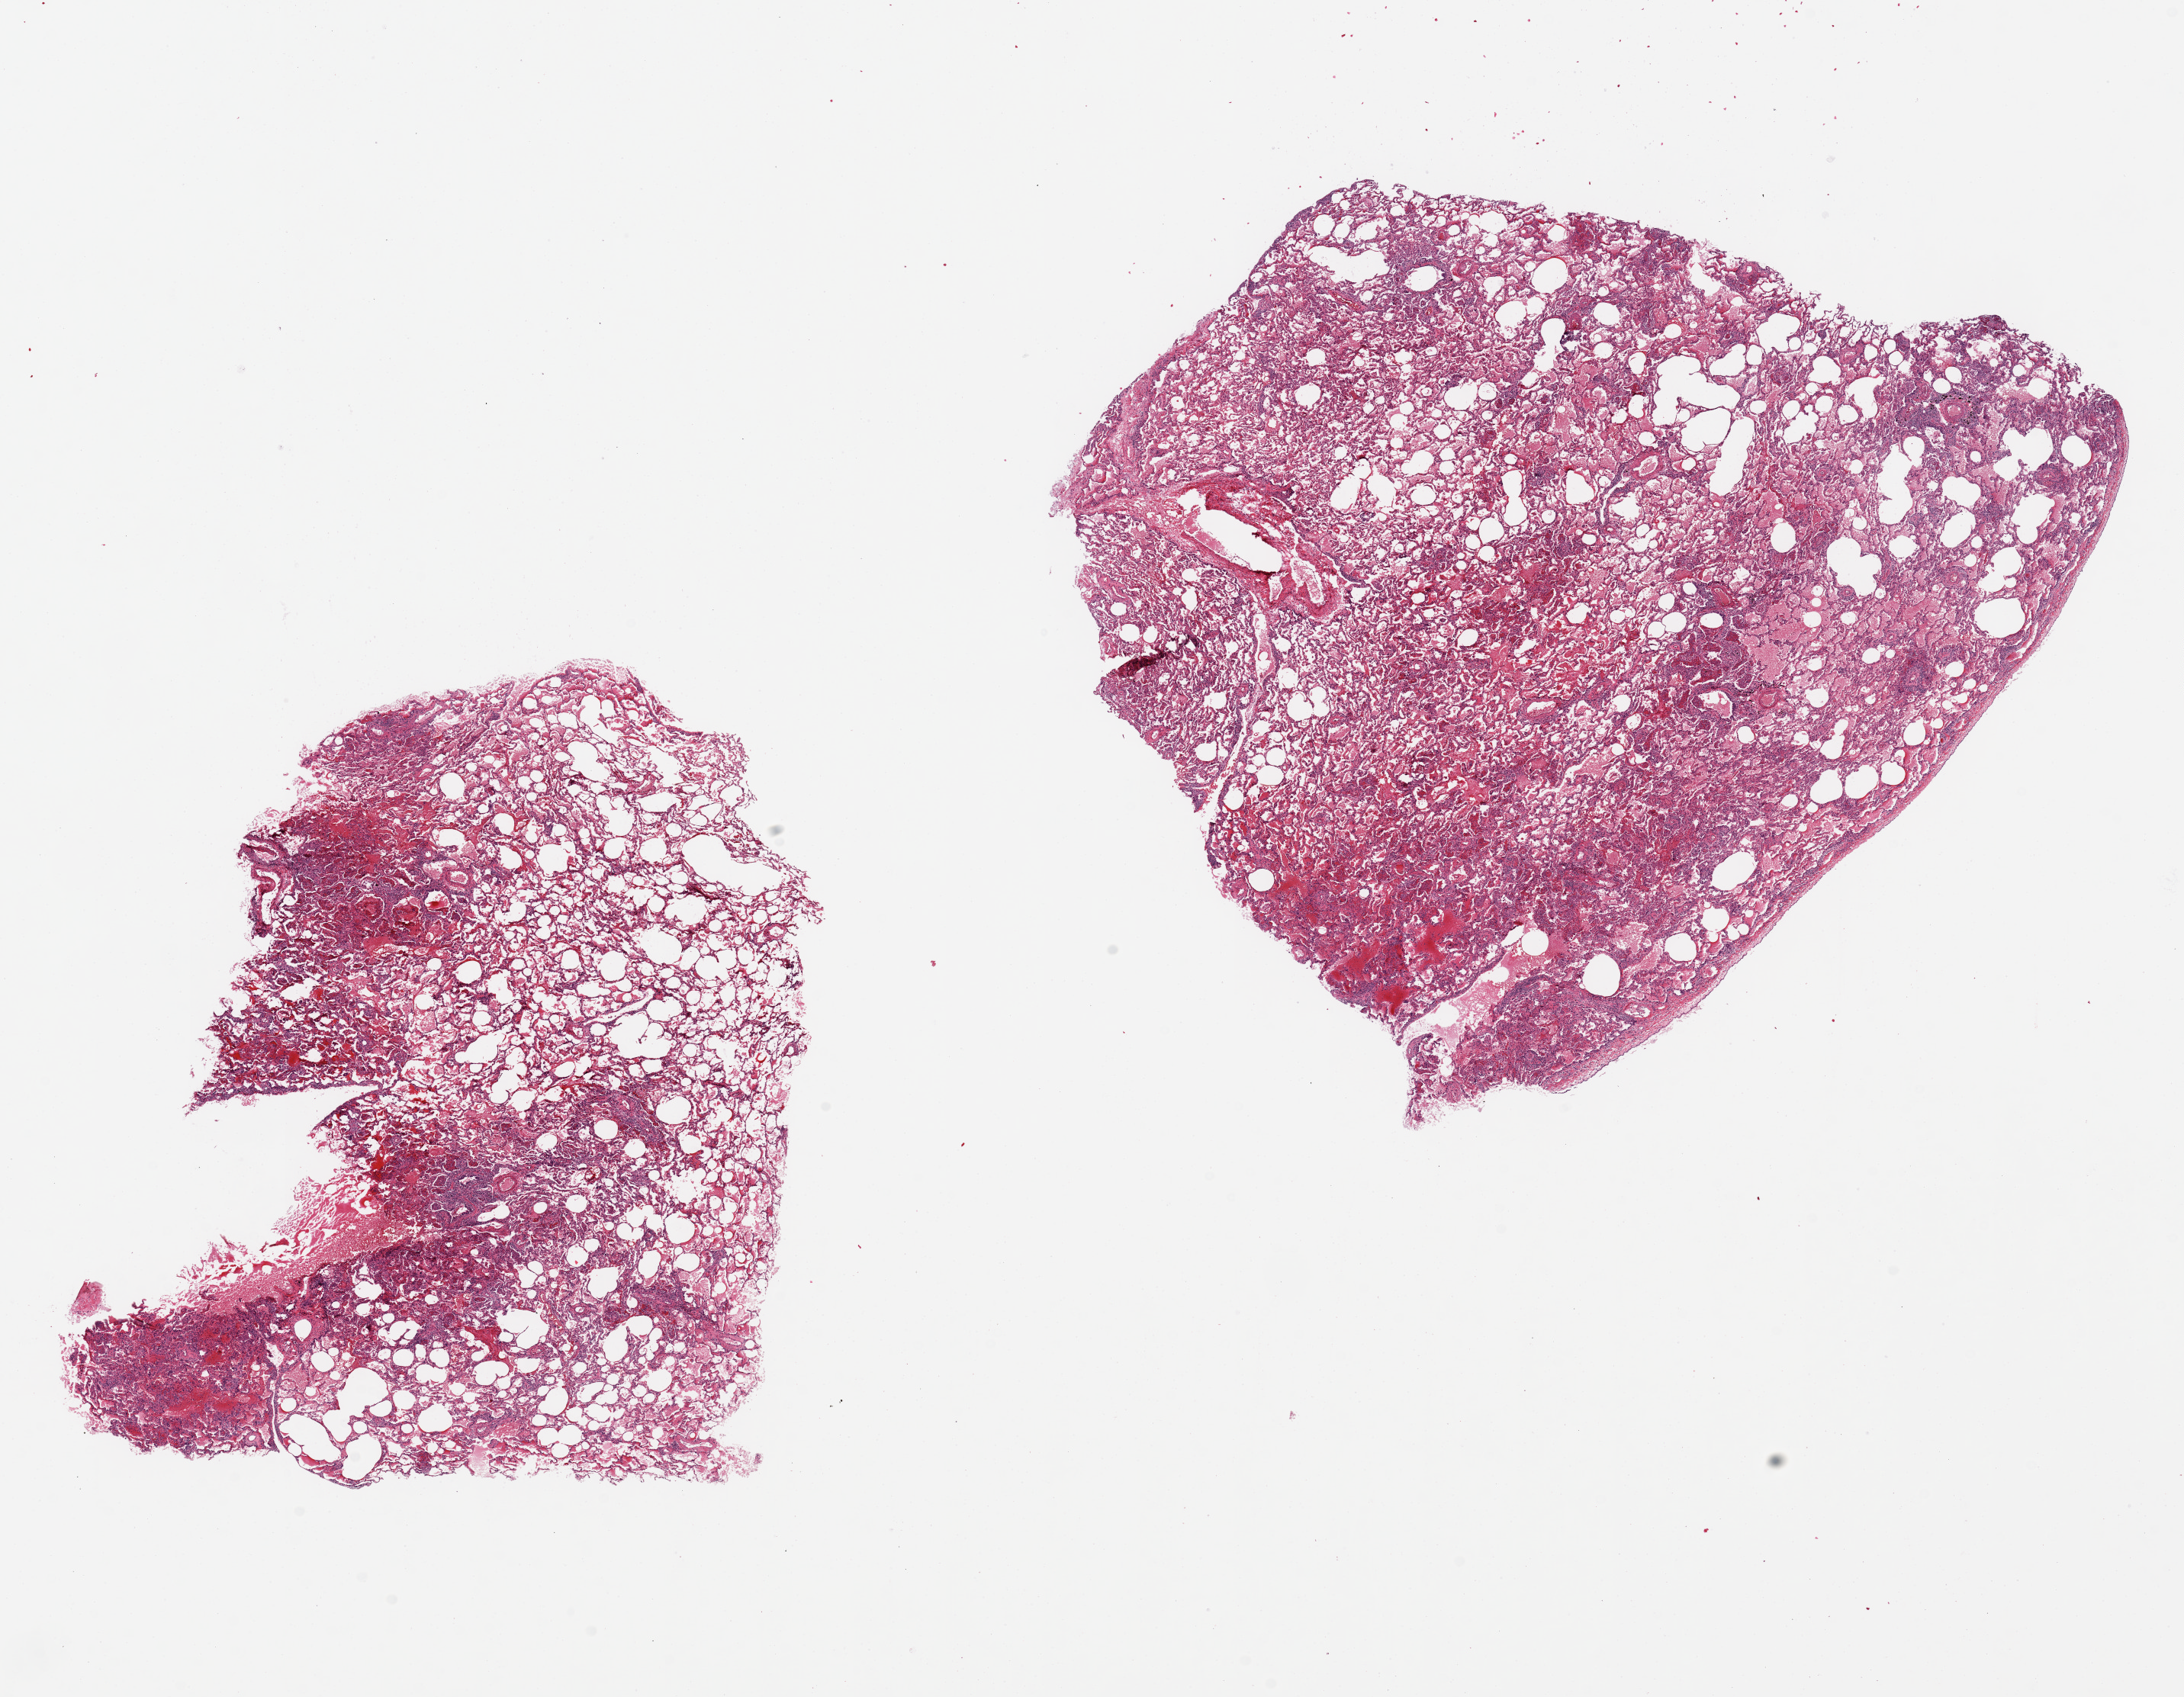
Whole-slide image, H&E stain, brightfield — shown as a low-resolution overview of the whole scanned area (about 22.6 x 17.6 mm, from a 20x scan), PAXgene-fixed, paraffin-embedded tissue, target tissue: lung, donor tissue sample. Donor: female.
Pathologist's review note for this sample: 2 pieces, 9x7 & 10.5x8mm; patchy hemorrhagic acute/chronic pneumonia/necrotiziing.